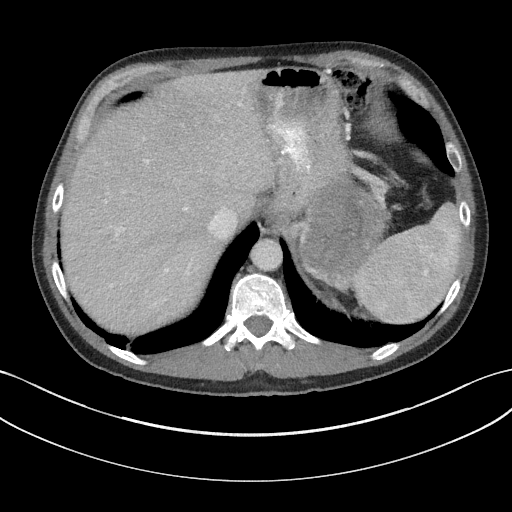
Contrast-enhanced abdominal CT, one axial slice. Position 129 of 147 along the scan axis. Intravenous contrast given. Soft-tissue window (W 400 / L 40 HU). 3 mm slice thickness. 512 × 512 image matrix, field of view 384 × 384 mm. Patient: male, 58 years. From the clinical record (not read from this slice): diagnosis: adrenocortical carcinoma; tumour side: left adrenal; tumour size at pathology: 22 cm; Ki-67 index: 26 %; stage (as recorded): 2.
Structures marked on this image (semi-automatically segmented with operator editing):
- mass: bounding box <305,178,377,273> (left, top, right, bottom; pixels)